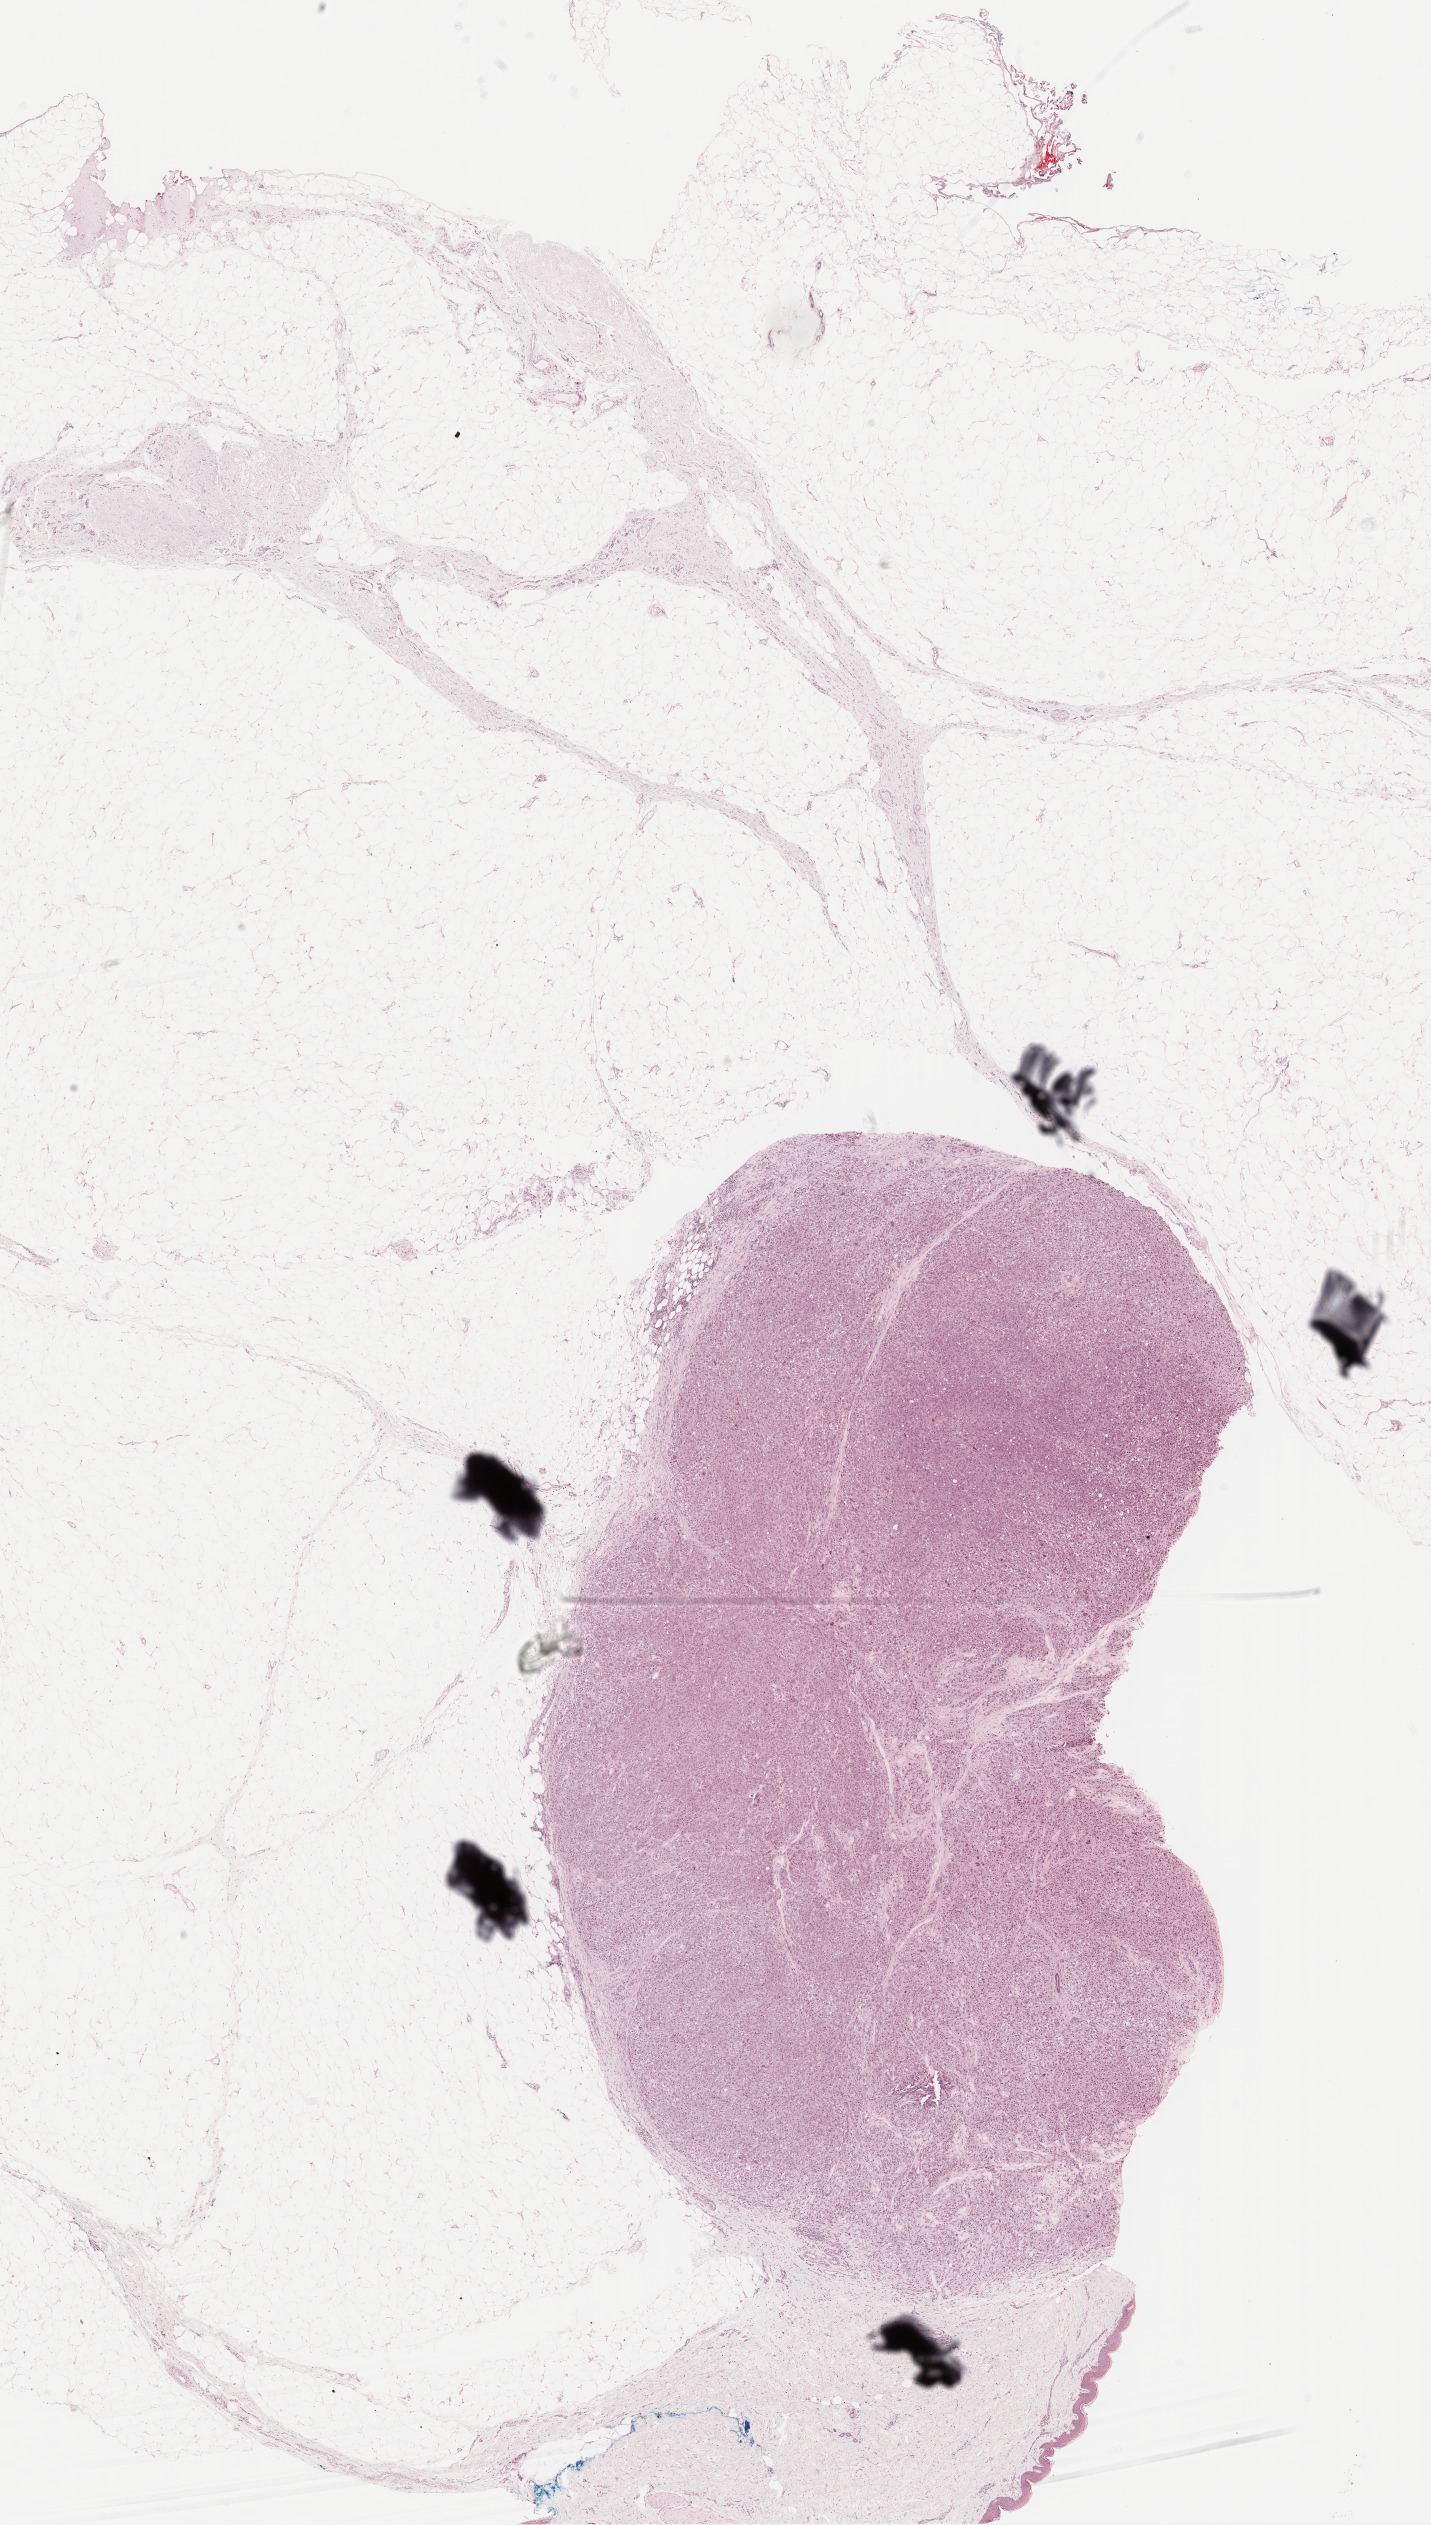
Hematoxylin and eosin (H&E) stained whole-slide image — whole scanned area (about 11.5 x 20.4 mm) shown as a low-resolution overview, formalin-fixed paraffin-embedded (FFPE) diagnostic section, metastatic tumour sample, sampled site: connective, subcutaneous and other soft tissues. Female, age 69 years at initial diagnosis.
This section: metastatic tumour tissue. Patient diagnosis: Malignant melanoma, NOS.